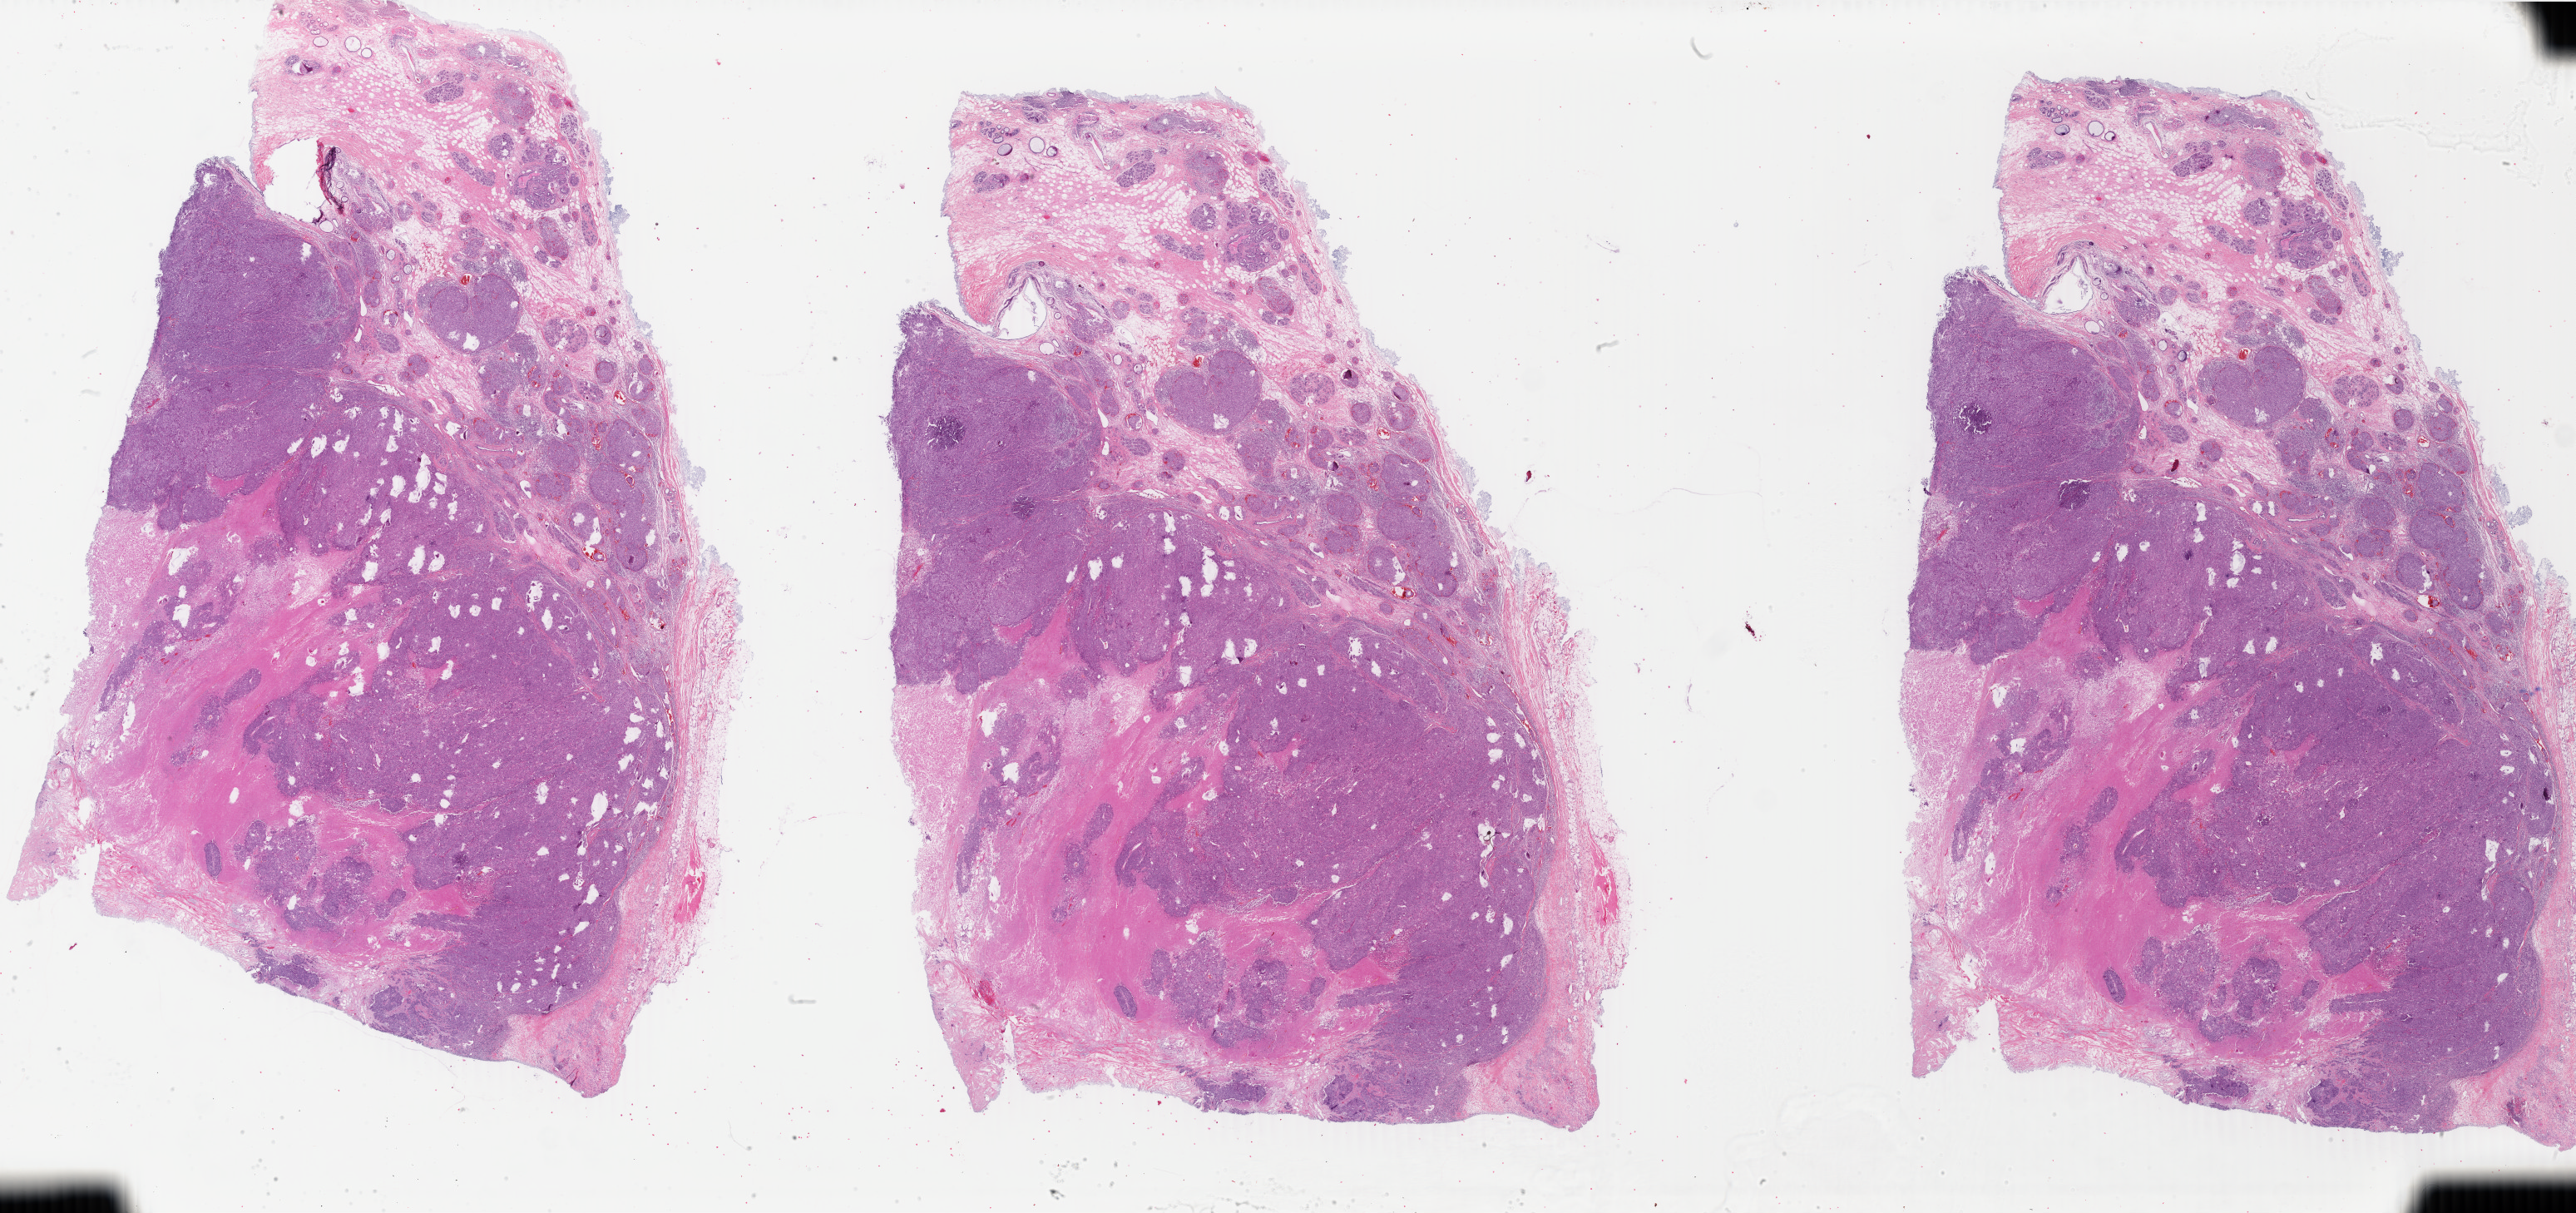
Whole-slide histology image, Hematoxylin and eosin (H&E) stained — whole scanned area (about 49.3 x 23.2 mm) shown as a low-resolution overview, FFPE section, sample: primary tumour, breast. Female patient; age at initial diagnosis 48 years.
• pathologic diagnosis: Infiltrating duct carcinoma, NOS
• laterality: left
• lymph nodes positive (case pathology): 16 of 21 examined